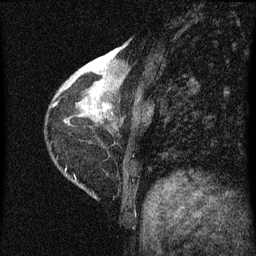
Breast MRI (dynamic contrast-enhanced), one sagittal slice; slice 17 of 60 in the series (ordered by position); dynamic contrast-enhanced series, image 2 of 3 at this slice position (ordered by acquisition); 1.5 T; TE 4.2 ms, TR 8 ms; 2 mm slice thickness; 256 × 256 image matrix, field of view 180 × 180 mm. Female patient, age 38 years.
Structures marked on this image (semi-automatically segmented with operator editing):
- analysis volume of interest (the breast-tissue region the enhancement analysis was run in; not a lesion): box from (x=67, y=44) to (x=144, y=131) px
- tumour enhancement mask (voxels above the 70 % enhancement threshold inside the analysis volume of interest): (x=67, y=68)–(x=110, y=113)